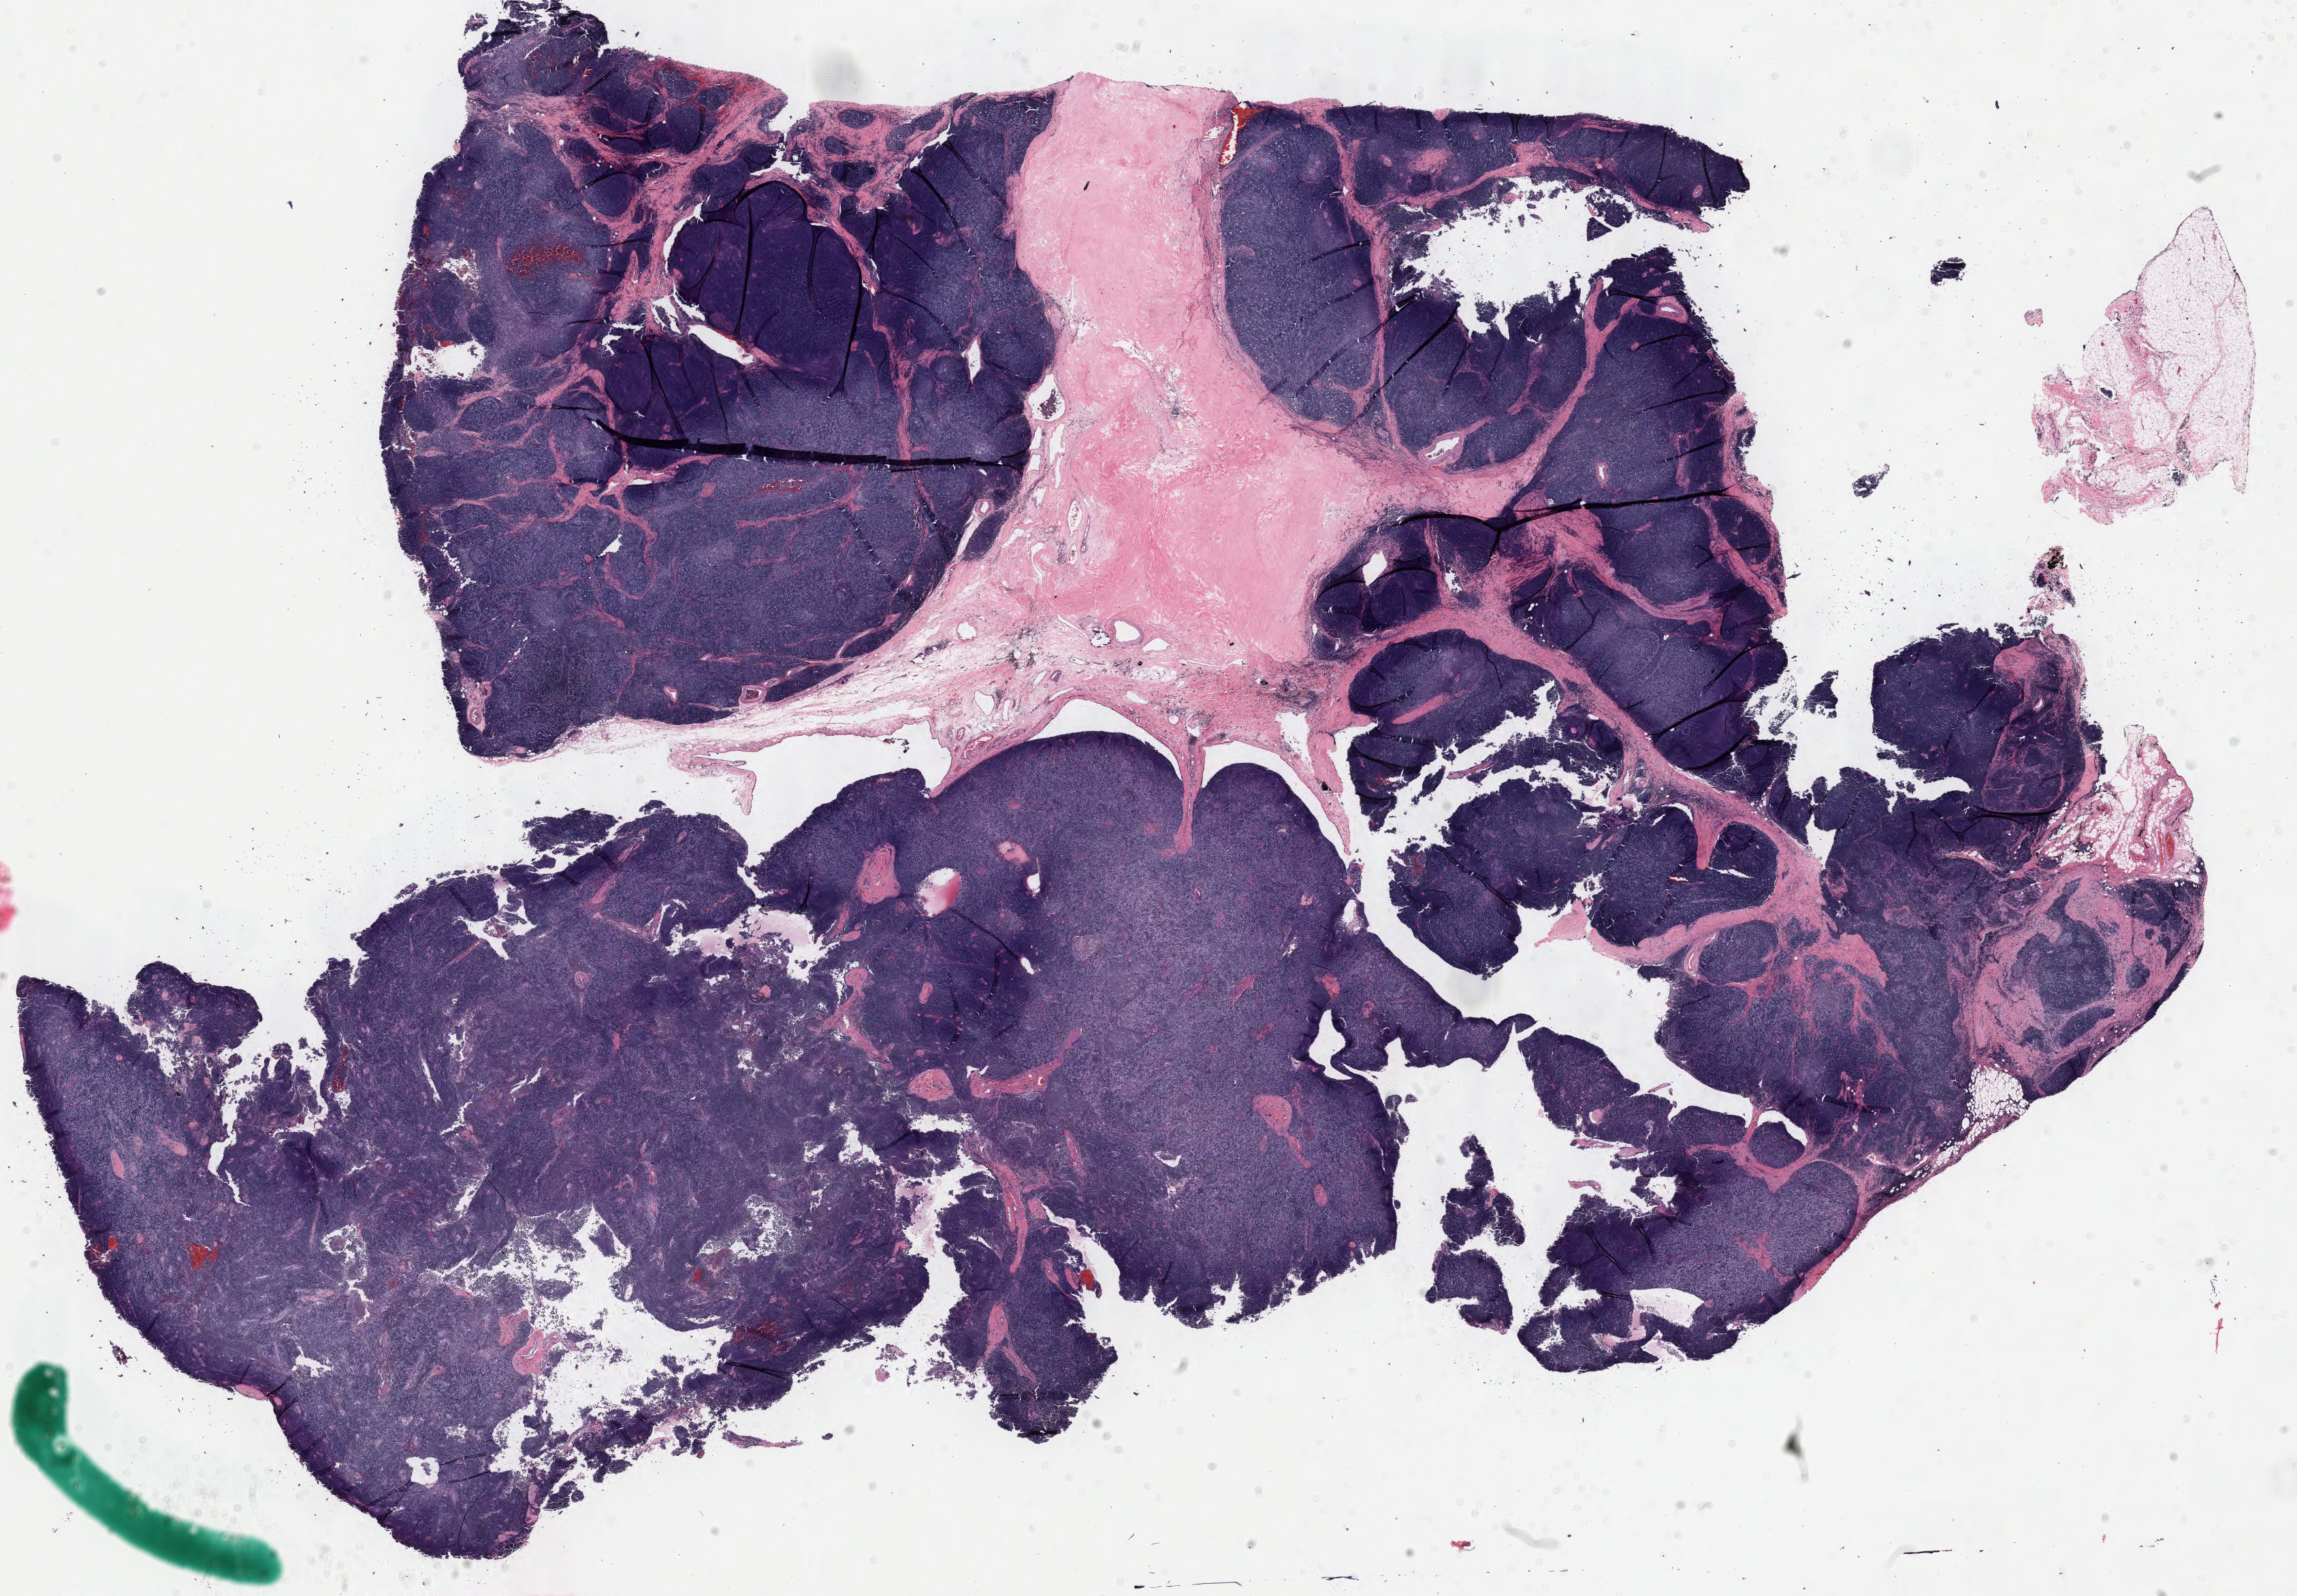
H&E-stained whole-slide image — whole scanned area (about 26.8 x 18.6 mm, from a 40x scan) shown as a low-resolution overview, formalin-fixed paraffin-embedded (FFPE) diagnostic section, thymus, primary tumour sample. Male, age 44 years at initial diagnosis.
Diagnosis: Thymoma, type B2, malignant.